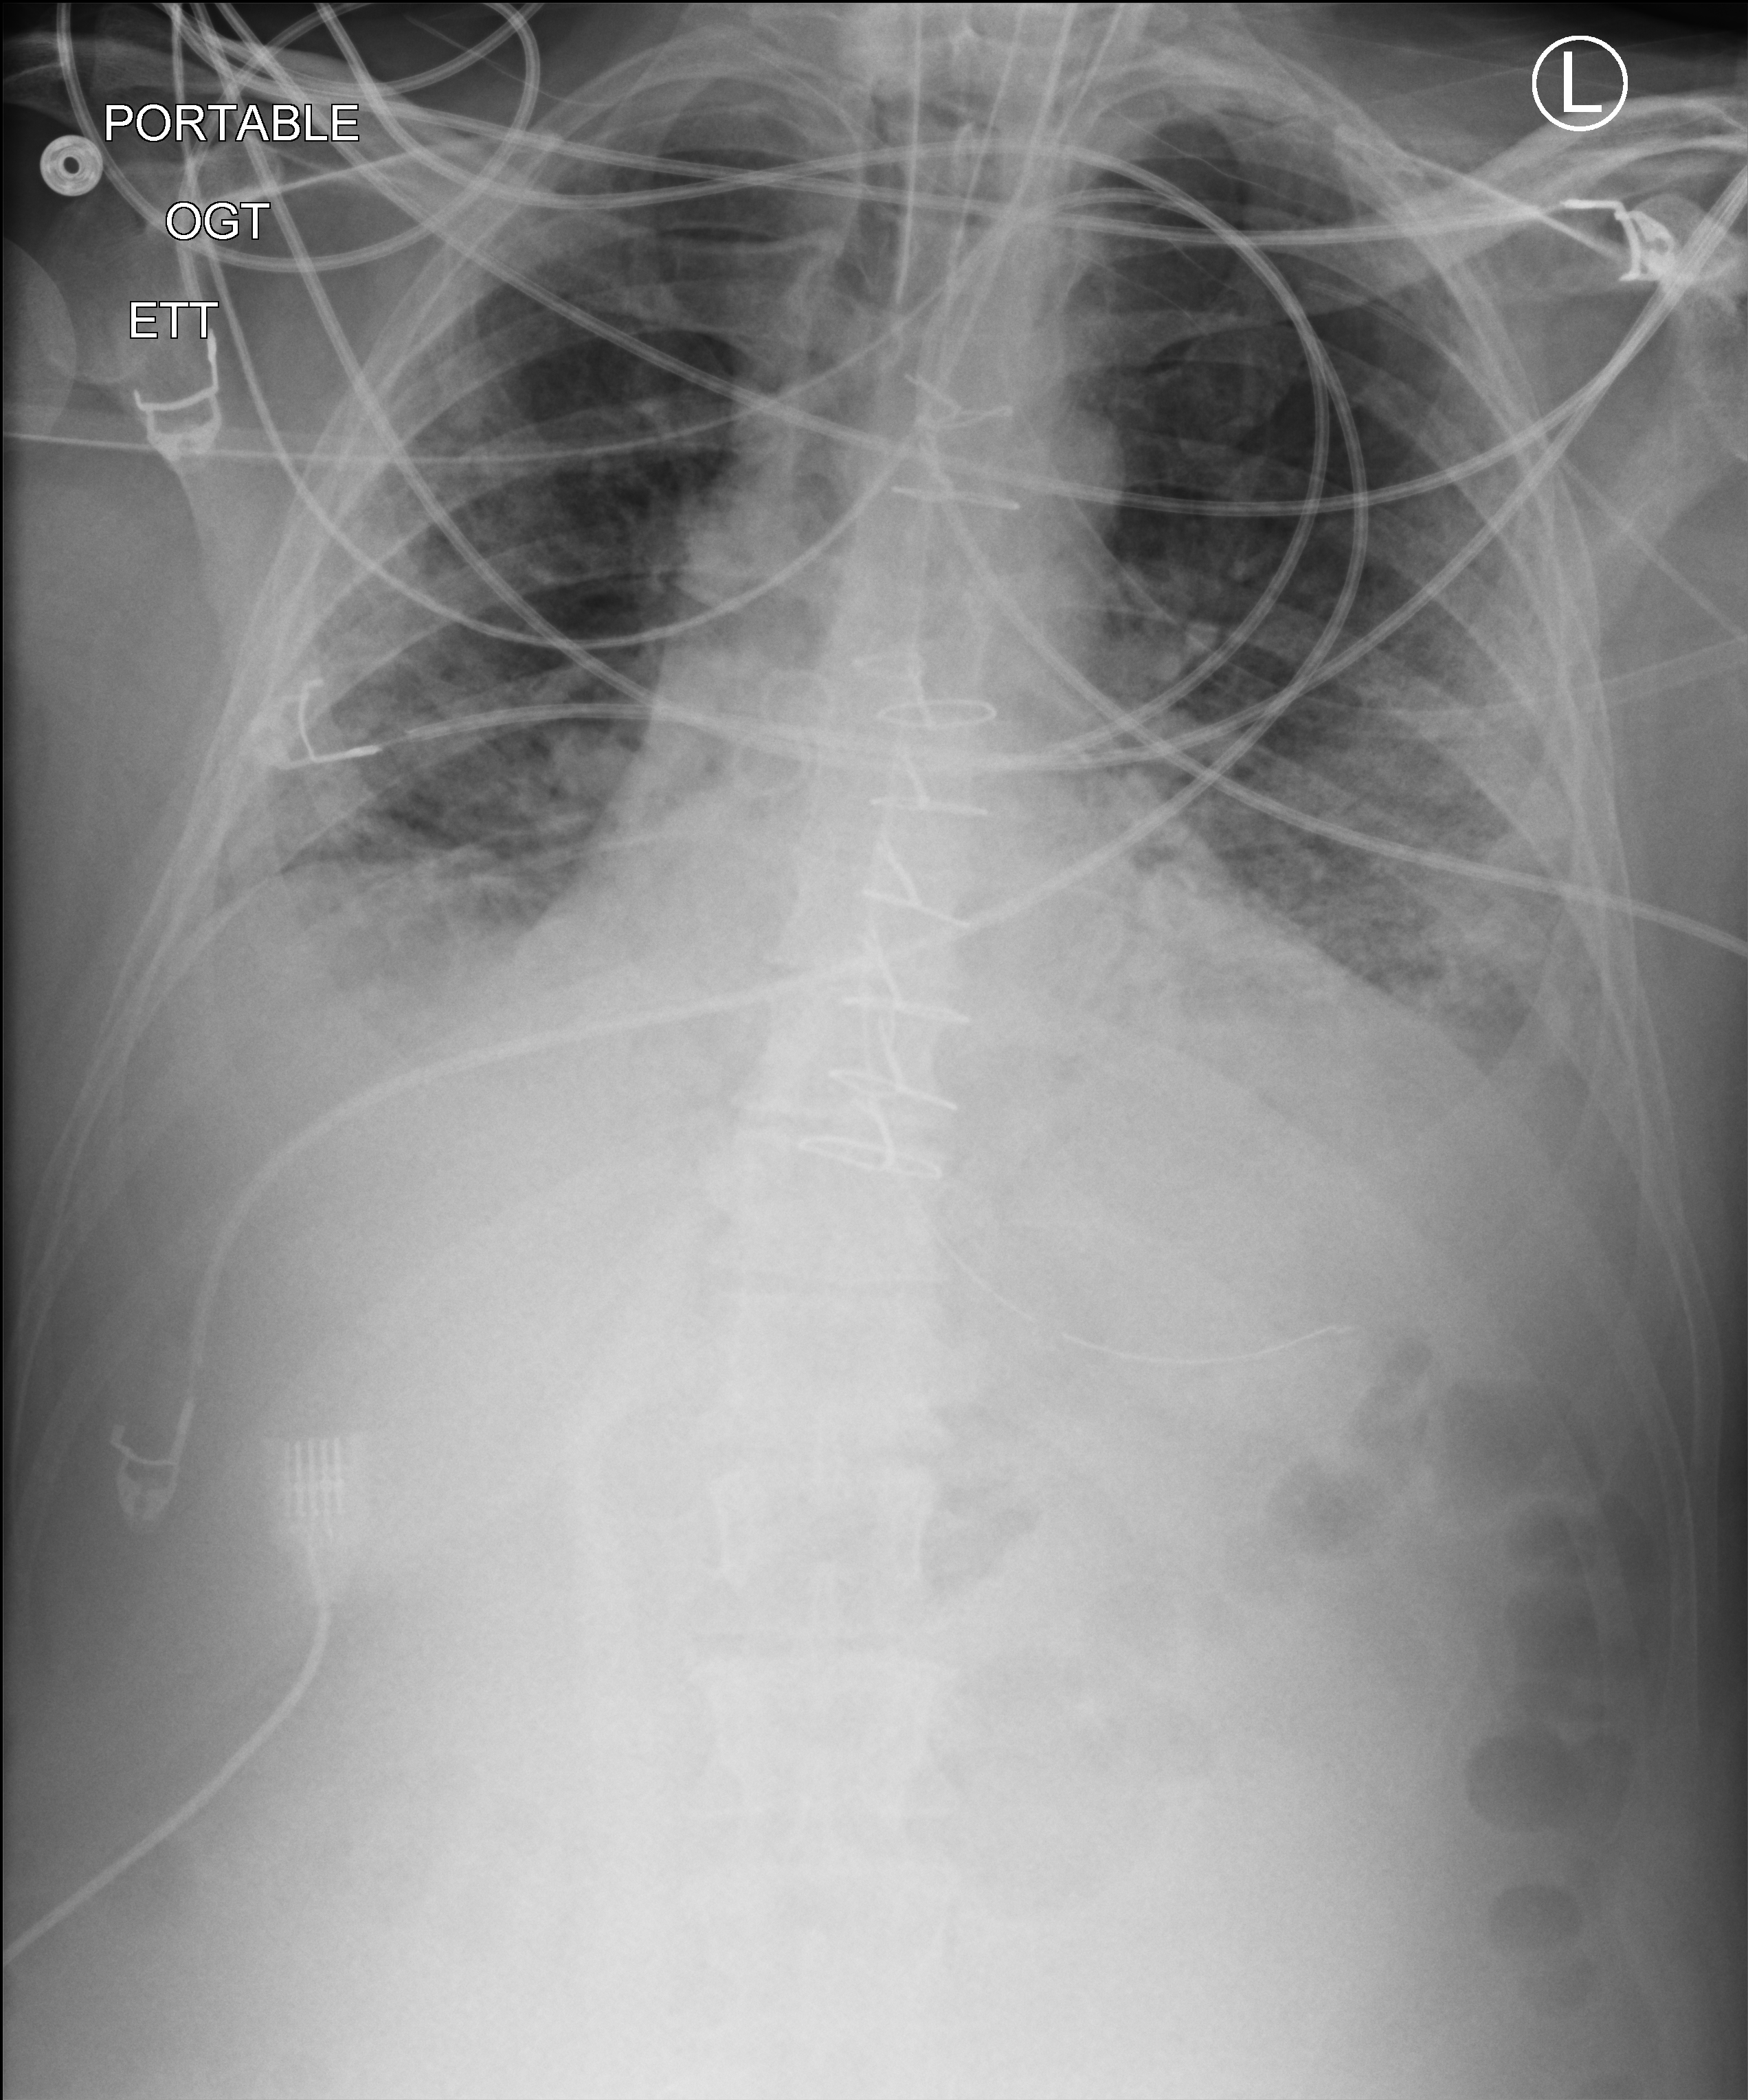
Chest X-ray (portable), anteroposterior (AP) projection. Patient hospitalised with COVID-19; male, aged 18–59 years.
Admission-level facts for this patient (not findings on this image; timing relative to this image not recorded): admitted to intensive care during this hospital stay: yes; mechanically ventilated during this hospital stay: yes.